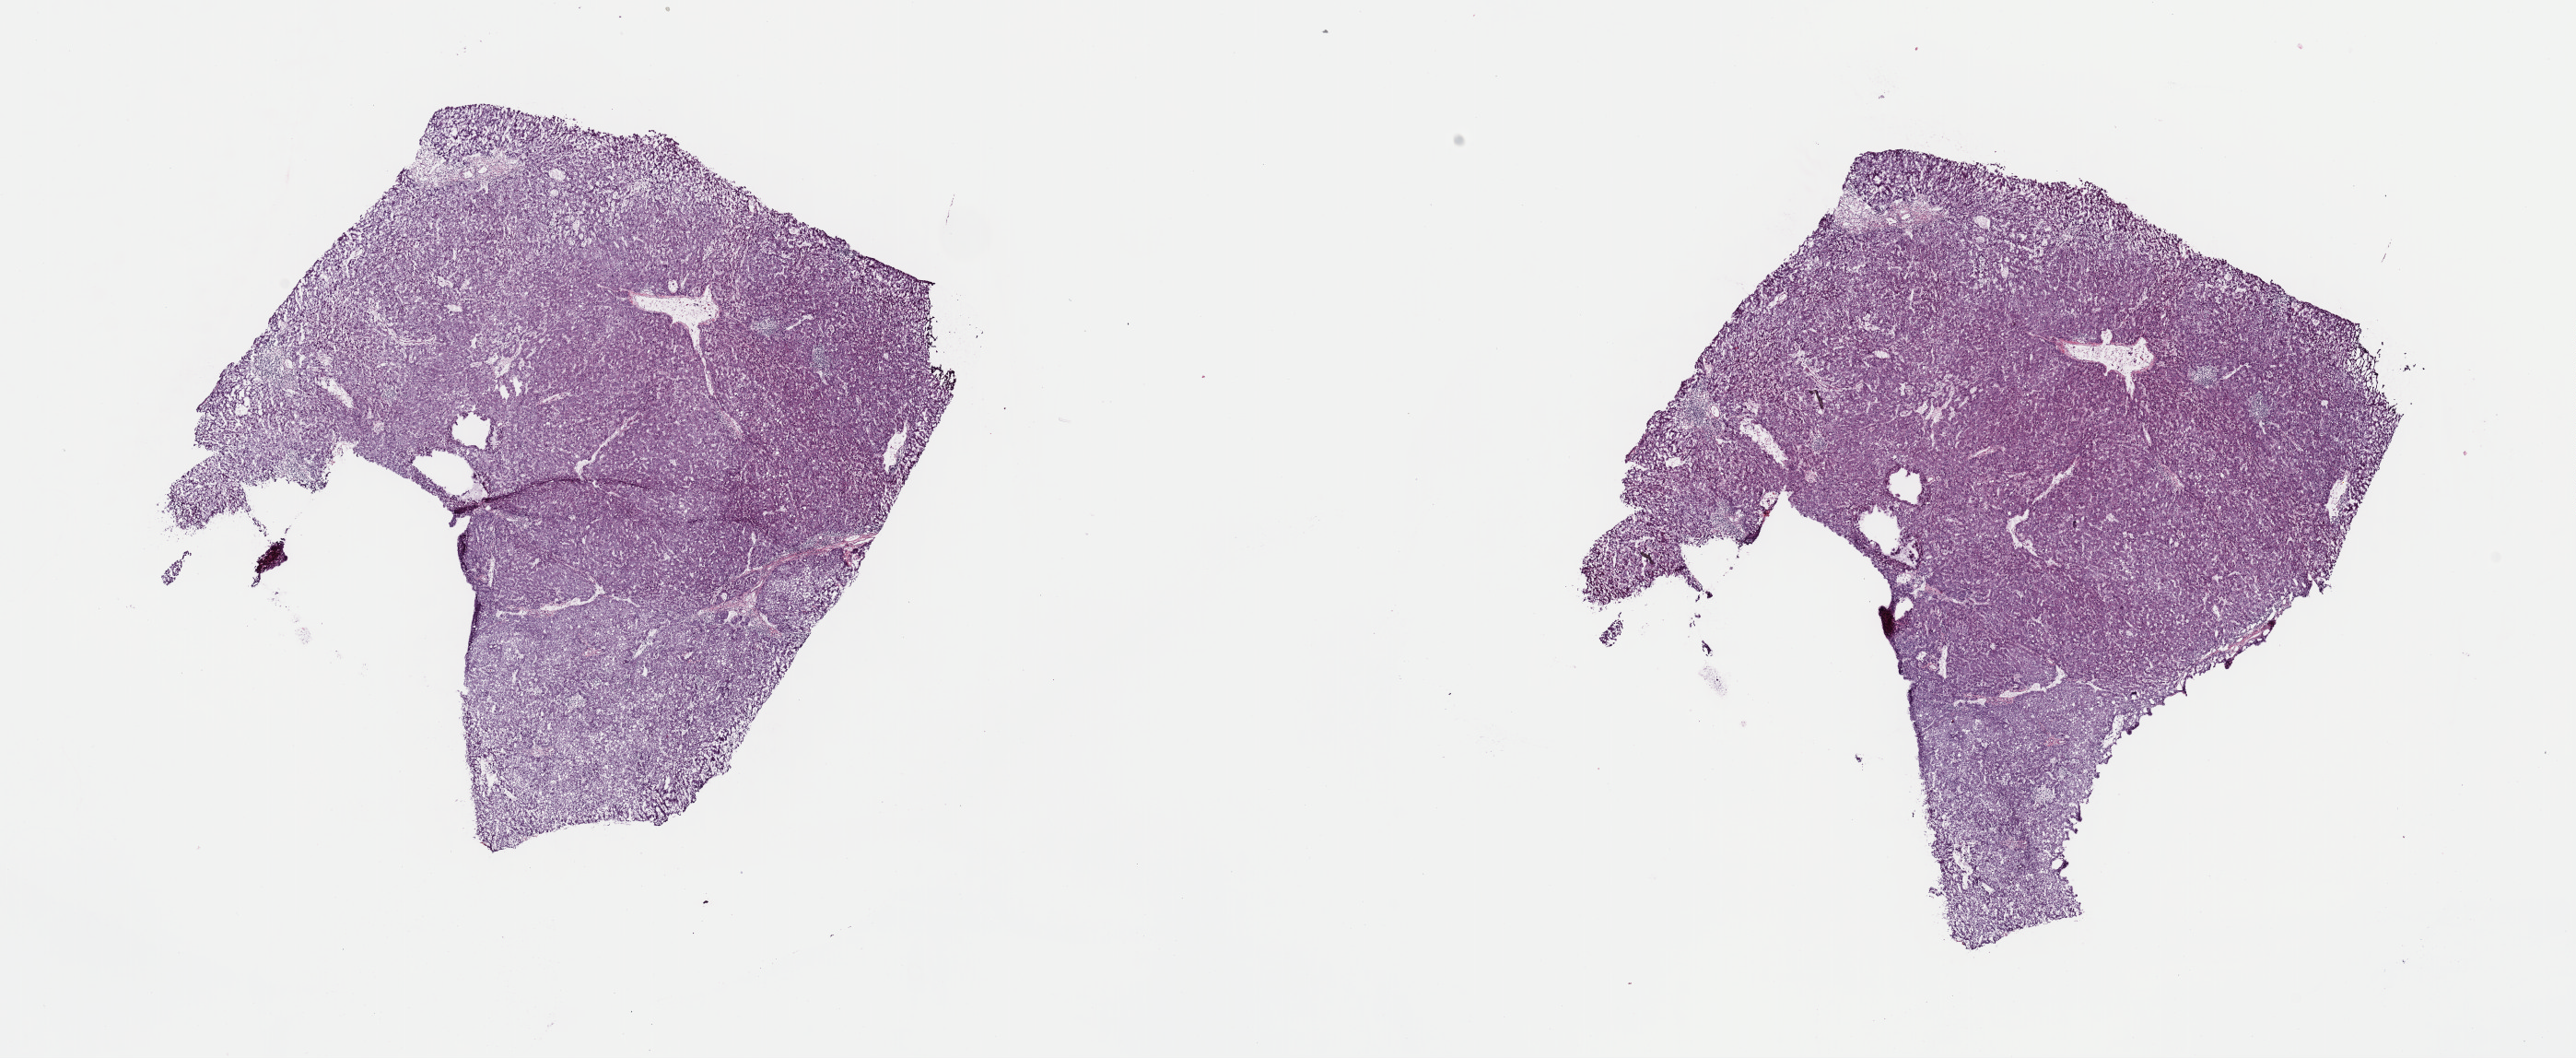
Digitized H&E-stained tissue section (whole slide) — a low-resolution overview of the entire scanned area, about 22.1 x 9.1 mm. Frozen section from the top of the tissue portion. Sample: primary tumour, liver. Male patient; age at initial diagnosis 67 years. Histologic grade: G2 (moderately differentiated). Composition of this section per pathologist review: tumour cells 95%, tumour nuclei 95%, normal cells 0%, stromal cells 5%, necrosis 0%. Inflammatory infiltration, as recorded: lymphocyte infiltration 10%, monocyte infiltration 0%, neutrophil infiltration 0%.
TNM: T2 NX M0. Histologic diagnosis: Hepatocellular carcinoma, NOS. AJCC pathologic stage: II.